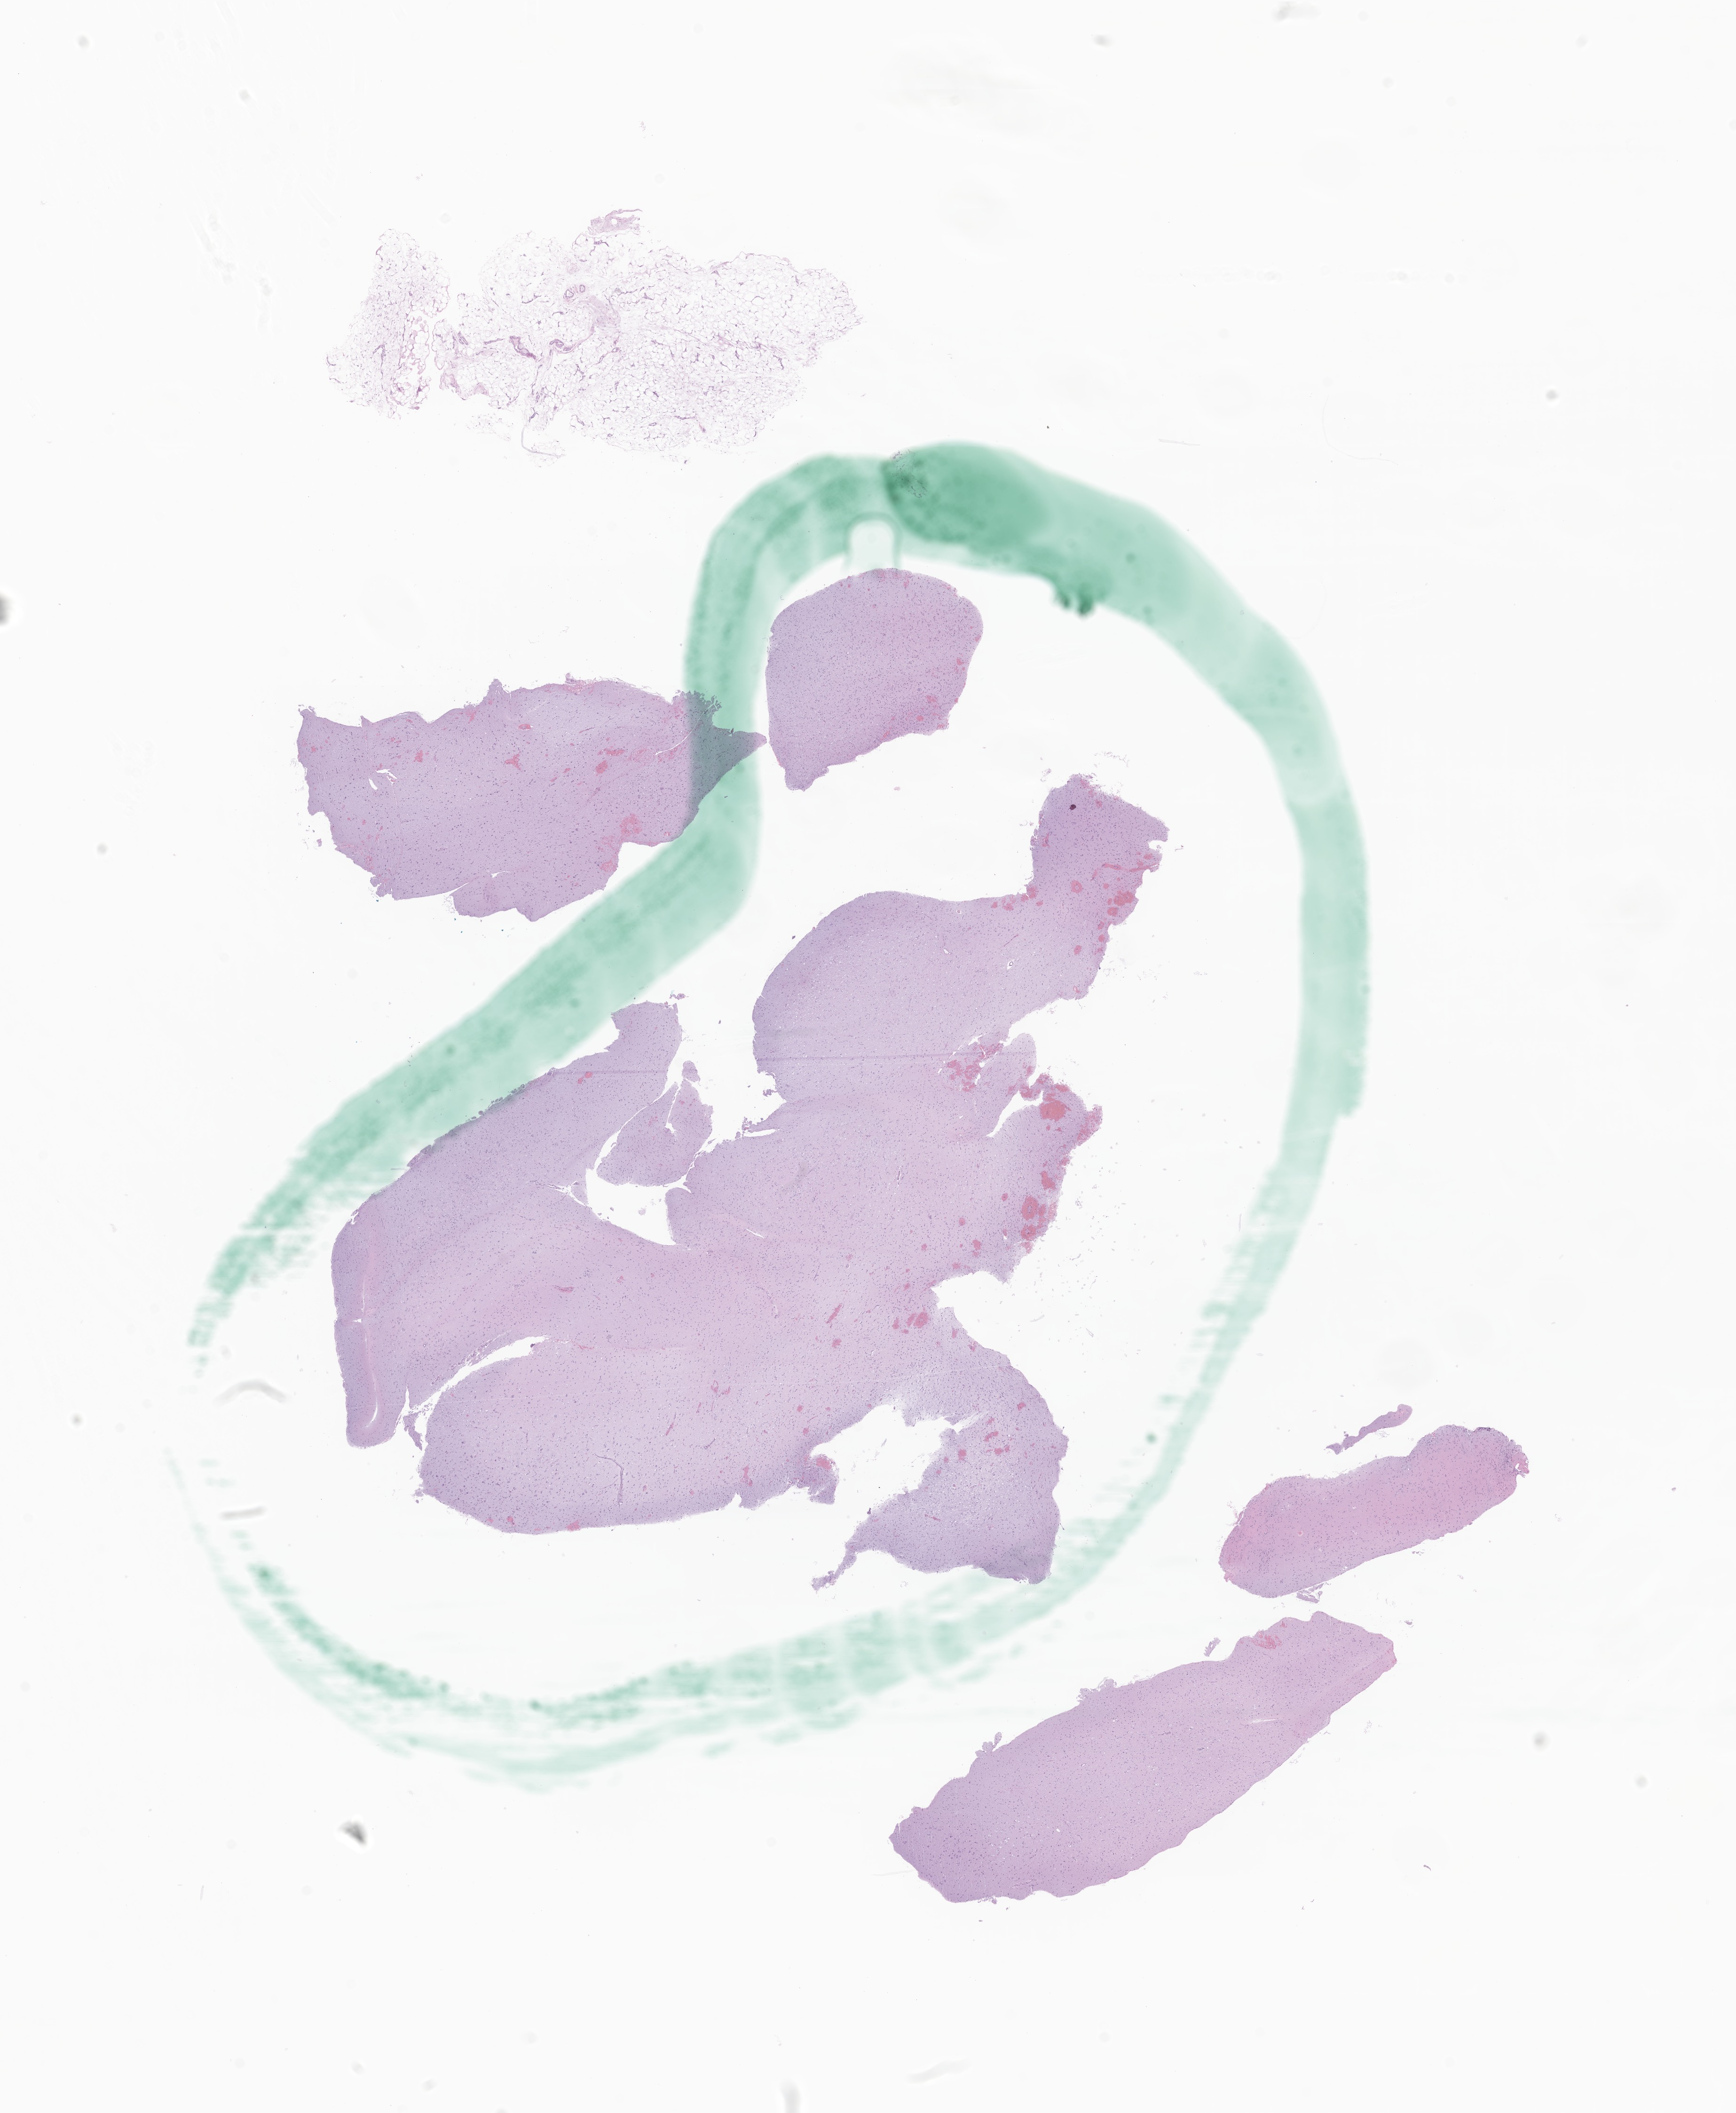
Digitized hematoxylin and eosin (H&E)-stained section of tumor tissue from the temporal lobe — a low-resolution overview of the entire scanned area, about 15.6 x 18.9 mm. Formalin-fixed, paraffin-embedded (FFPE) tissue. Patient: male, age 715 days.
Diagnosis (ICD-O-3 morphology term): Glioma, malignant.